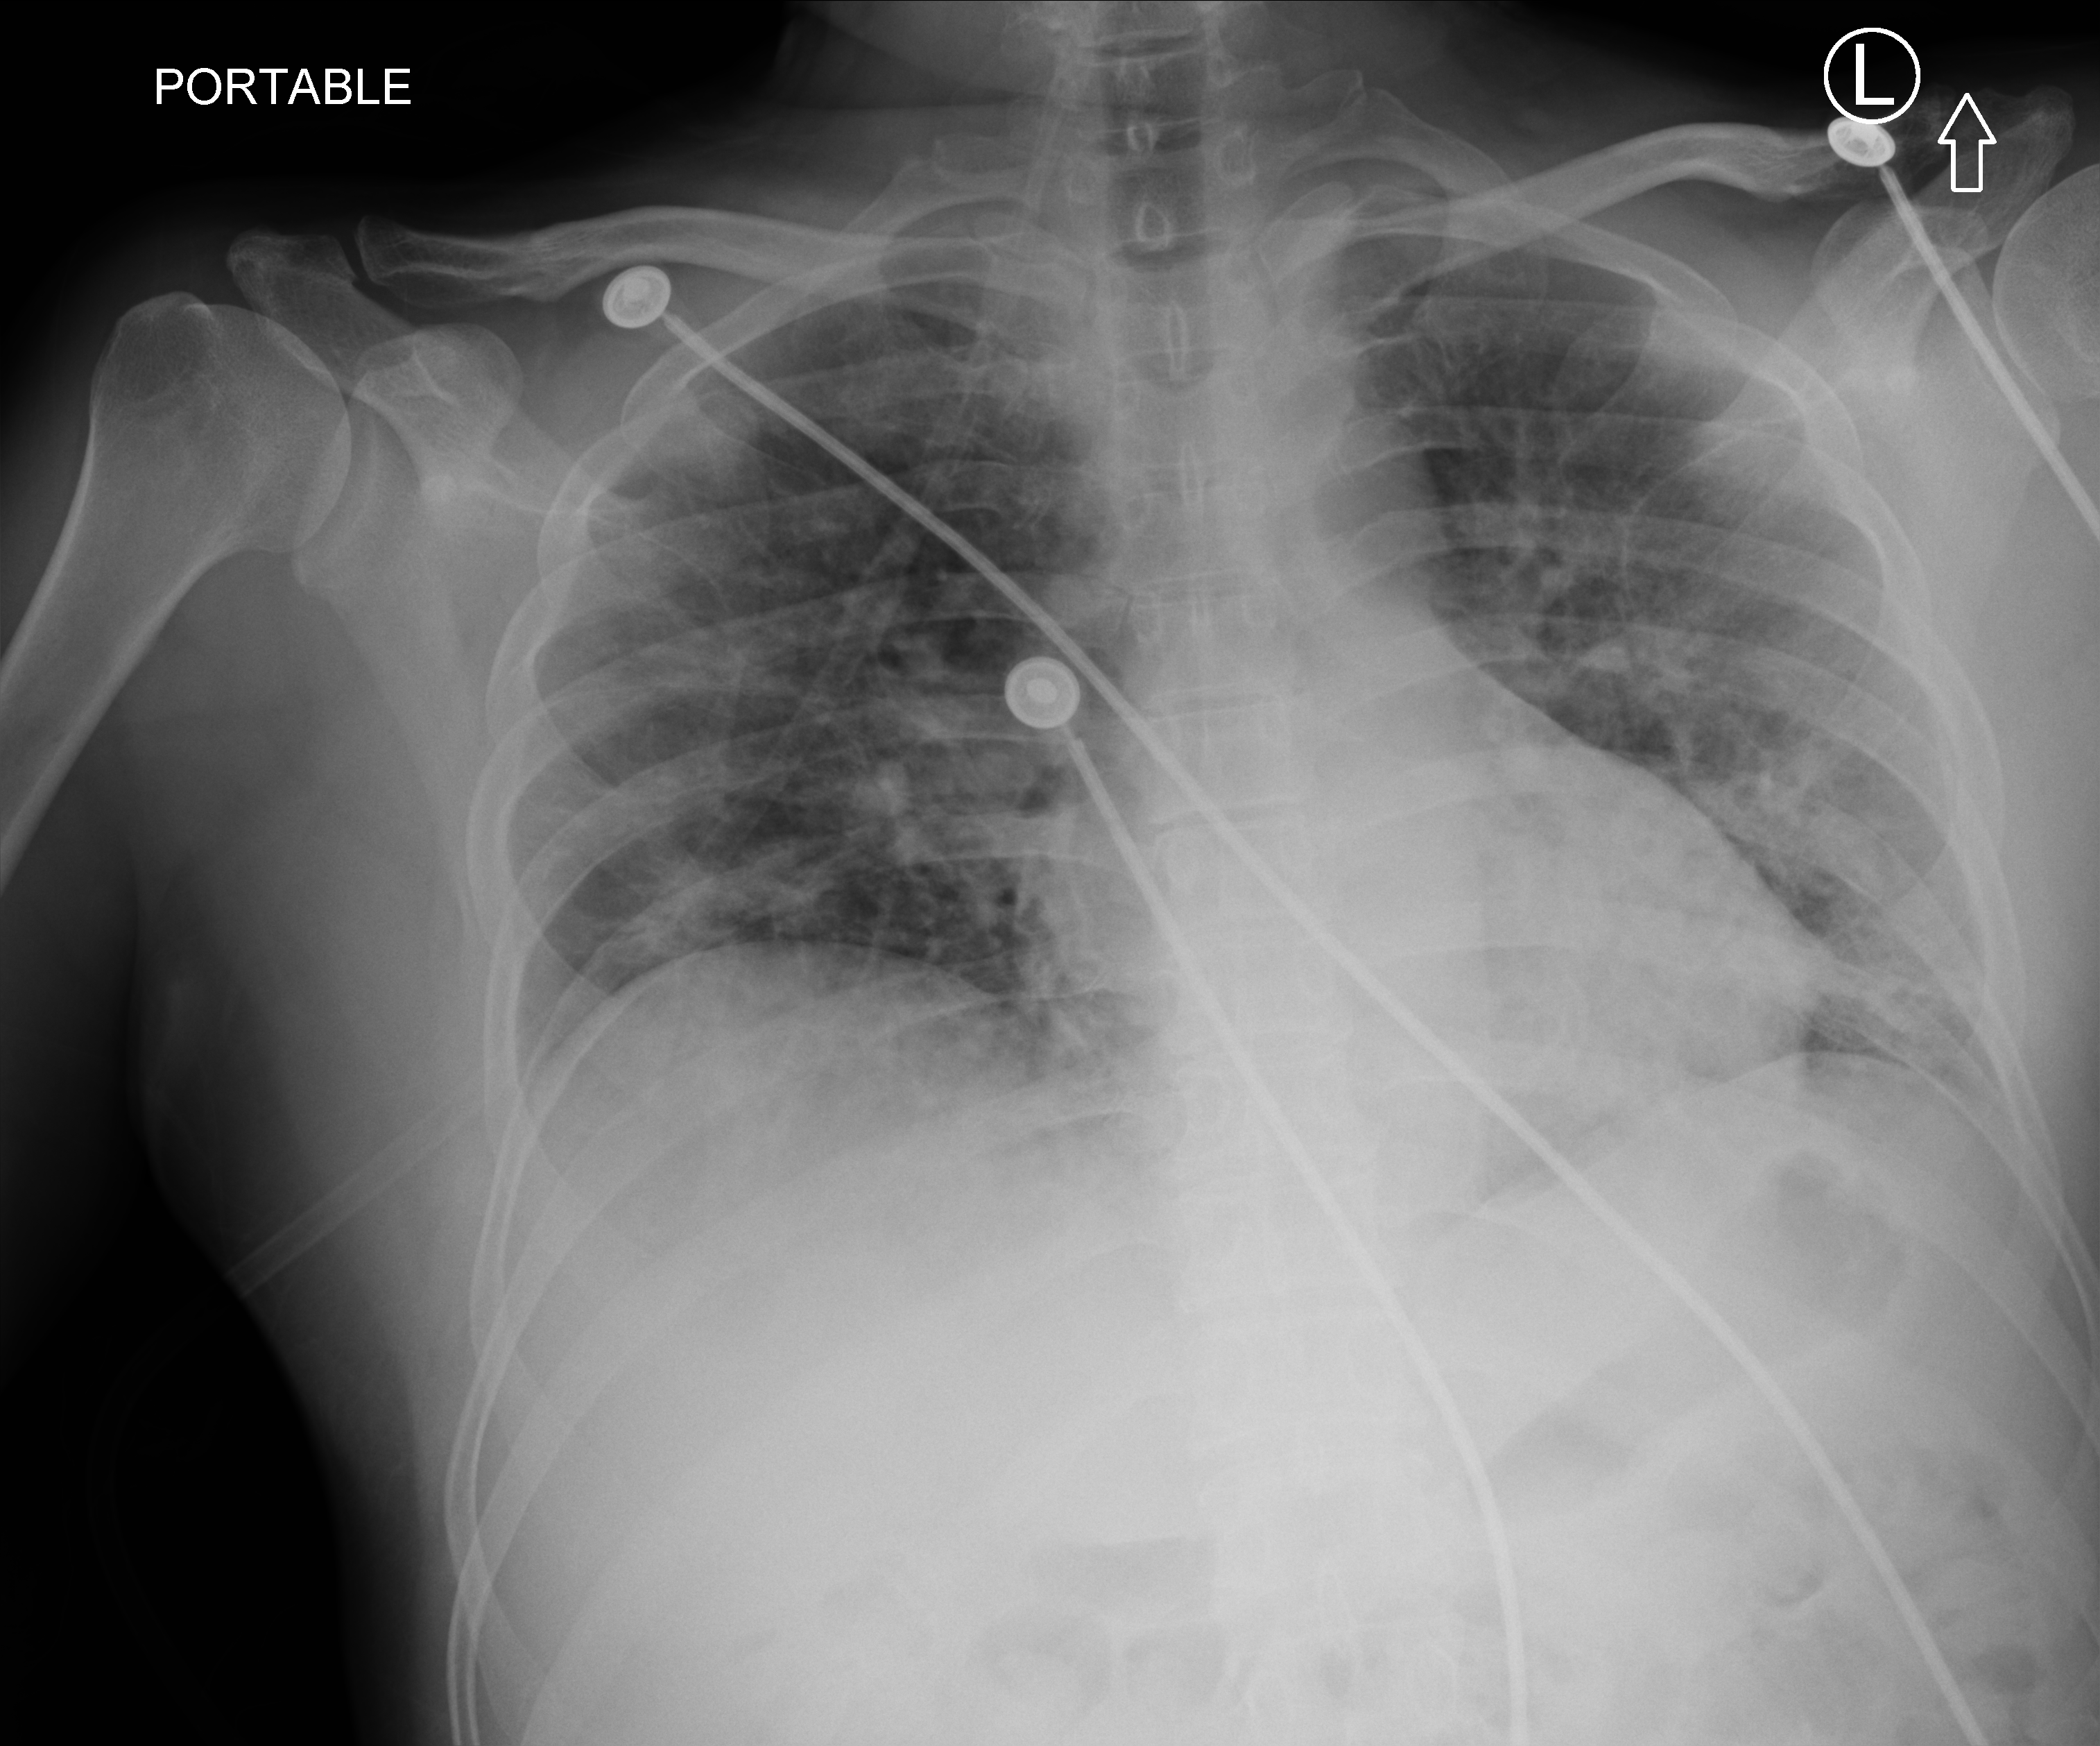
Bedside chest radiograph (computed radiography), anteroposterior (AP) projection. Male patient hospitalised with COVID-19, age 18–59 years.
Hospital-stay facts (about this admission, not read from this image; timing relative to this image not recorded): hypertension (admission record): no; COPD (admission record): no.